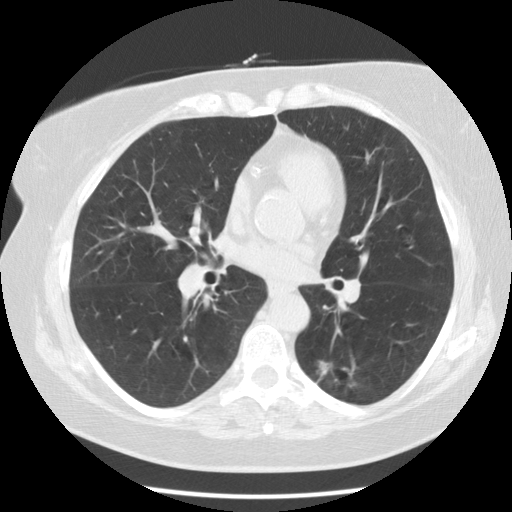
Axial slice from a low-dose chest CT screening exam. Second annual screen. Lung window (W 1500 / L -600 HU). 512 × 512 image matrix. Female participant, aged 59 years at enrolment.
Lesion marked by an expert reader, box from (x=296, y=343) to (x=373, y=410) px. The screening reader recorded 5 non-calcified nodules or masses ≥4 mm on this exam; which of them this box marks is not recorded. Lung cancer was diagnosed 343 days after this screen: adenocarcinoma, NOS, left lower lobe, poorly differentiated (G3), stage IA (AJCC 6th edition), 15 mm at pathology.